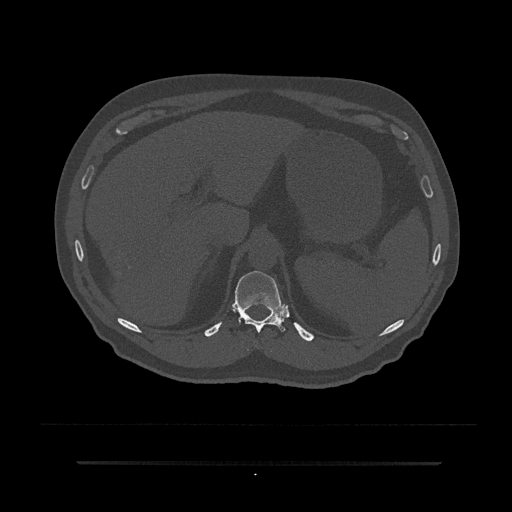
CT including the spine, one axial slice. Position 268 of 797 along the scan axis. Bone window (W 1800 / L 400 HU). 0.5 mm slice thickness. 512 × 512 image matrix. Patient: male, 59 years. Case-level facts recorded for this patient, not image findings: primary cancer: bile ducts; vertebrae with lytic lesions (as recorded): T10.
Outlined on this slice (semi-automatically segmented with operator editing):
- T11 vertebra: box from (x=233, y=271) to (x=285, y=333) px